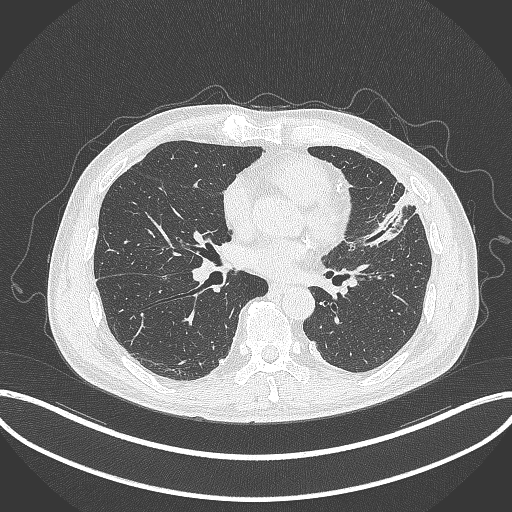
Chest CT, one axial slice. Position 152 of 382 along the scan axis. 120 kVp. Lung window (W 1500 / L -600 HU). 512 × 512 image matrix, field of view 415 × 415 mm. Male patient, age 64 years. From the clinical record (not read from this slice): clinical TNM (as recorded): T4 N1 M0.
Annotated regions visible in this slice (rectangle marked by the reading radiologist):
- lung tumour (recorded histology: adenocarcinoma): bounding box (x1, y1, x2, y2) in pixels: (361, 188, 429, 250)